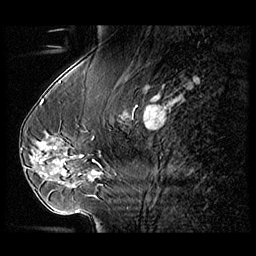
Breast MRI (dynamic contrast-enhanced), one sagittal slice. Slice 44 of 104 in the series (ordered by position). 3 images stored at this slice position (order not interpretable as contrast timing). 1.5 T. TE 1.3 ms, TR 5.5 ms. 3 mm slice thickness. 256 × 256 image matrix. Female patient, age 54 years. From the clinical record (not read from this slice): setting: breast cancer imaged before/during neoadjuvant chemotherapy; receptor status: HR-positive, HER2-negative.
Annotated regions visible in this slice (semi-automatic segmentation, software-assisted and operator-edited):
- analysis volume of interest (the breast-tissue region the enhancement analysis was run in; not a lesion): bounding box (x1, y1, x2, y2) in pixels: (28, 127, 104, 182)
- tumour enhancement mask (voxels above the 140 % enhancement threshold inside the analysis volume of interest): (54, 147, 64, 164)